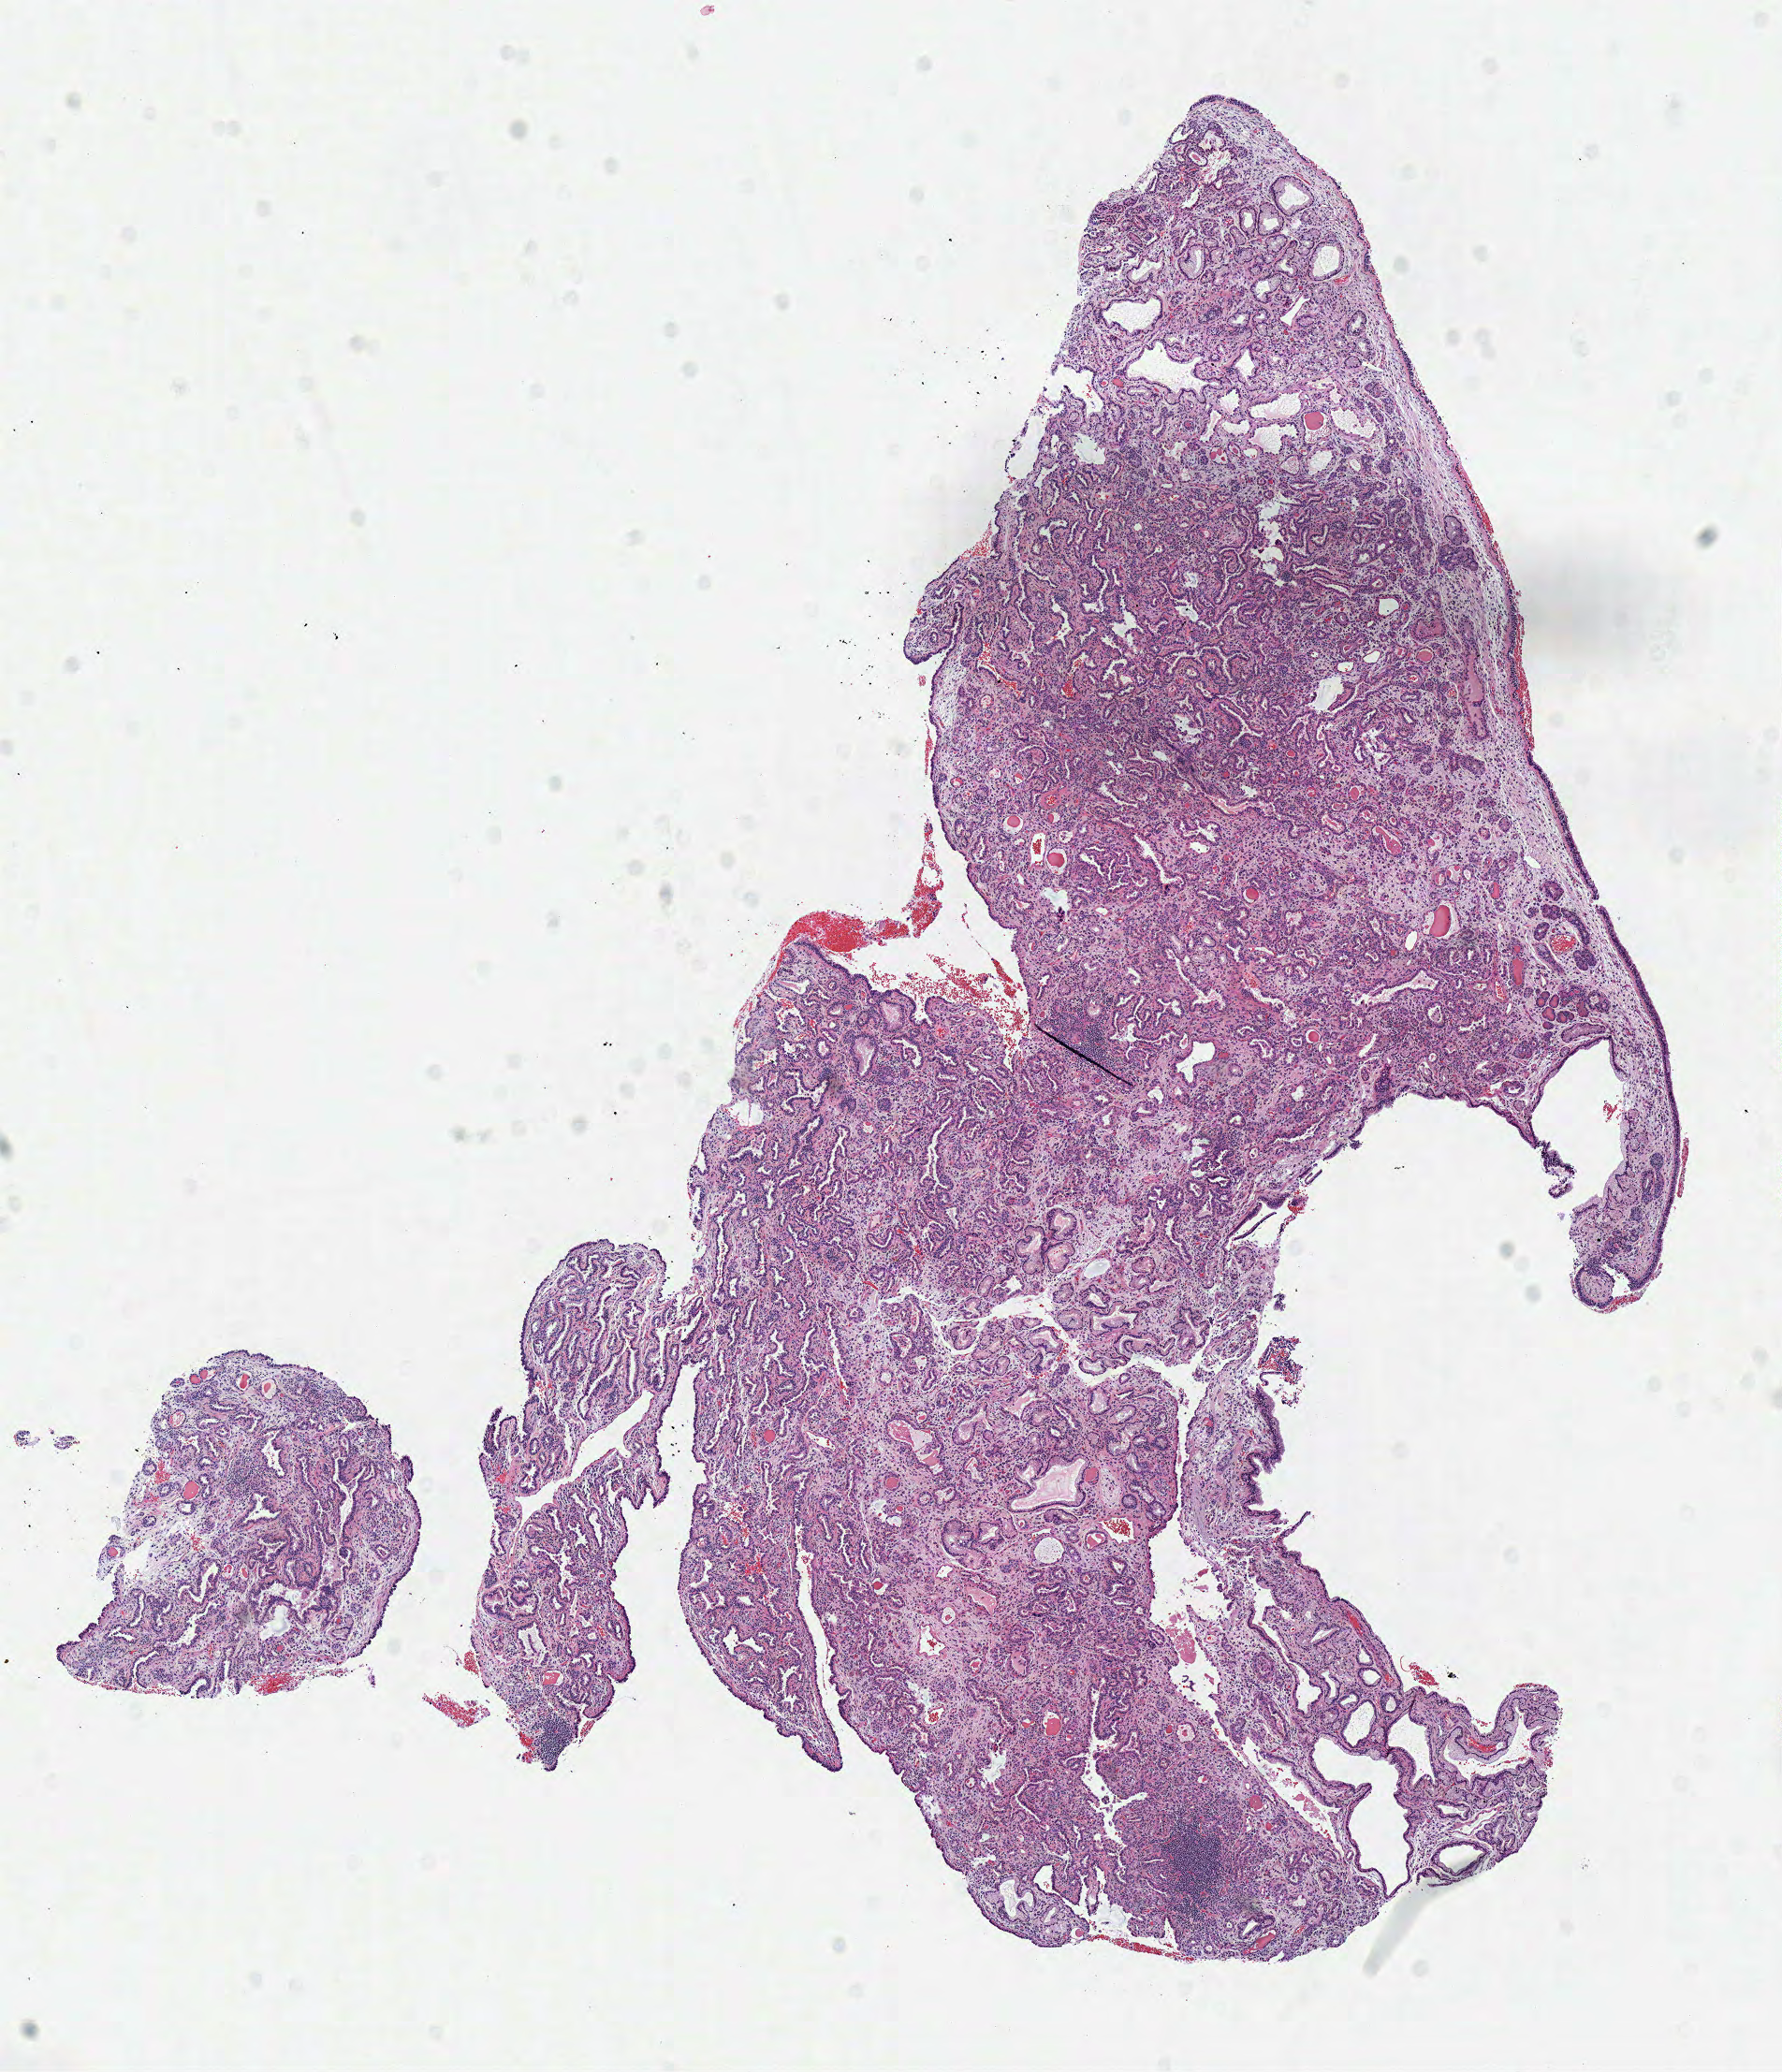
Whole-slide histology image, H&E-stained, a low-resolution overview of the entire scanned area, about 7.5 x 8.7 mm (acquisition: 40x scan); frozen section from the top of the tissue portion; lung, primary tumour sample. Patient: male, age at initial diagnosis 60 years. Pathologist review of this section (percent, as recorded): tumour cells 90%, tumour nuclei 80%, normal cells 10%, stromal cells 0%, necrosis 0%. Infiltration values recorded for this section: lymphocyte infiltration 10%, monocyte infiltration 0%, neutrophil infiltration 0%.
* AJCC pathologic stage: IA (7th edition)
* histologic diagnosis: Mucinous adenocarcinoma (lower lobe, lung)